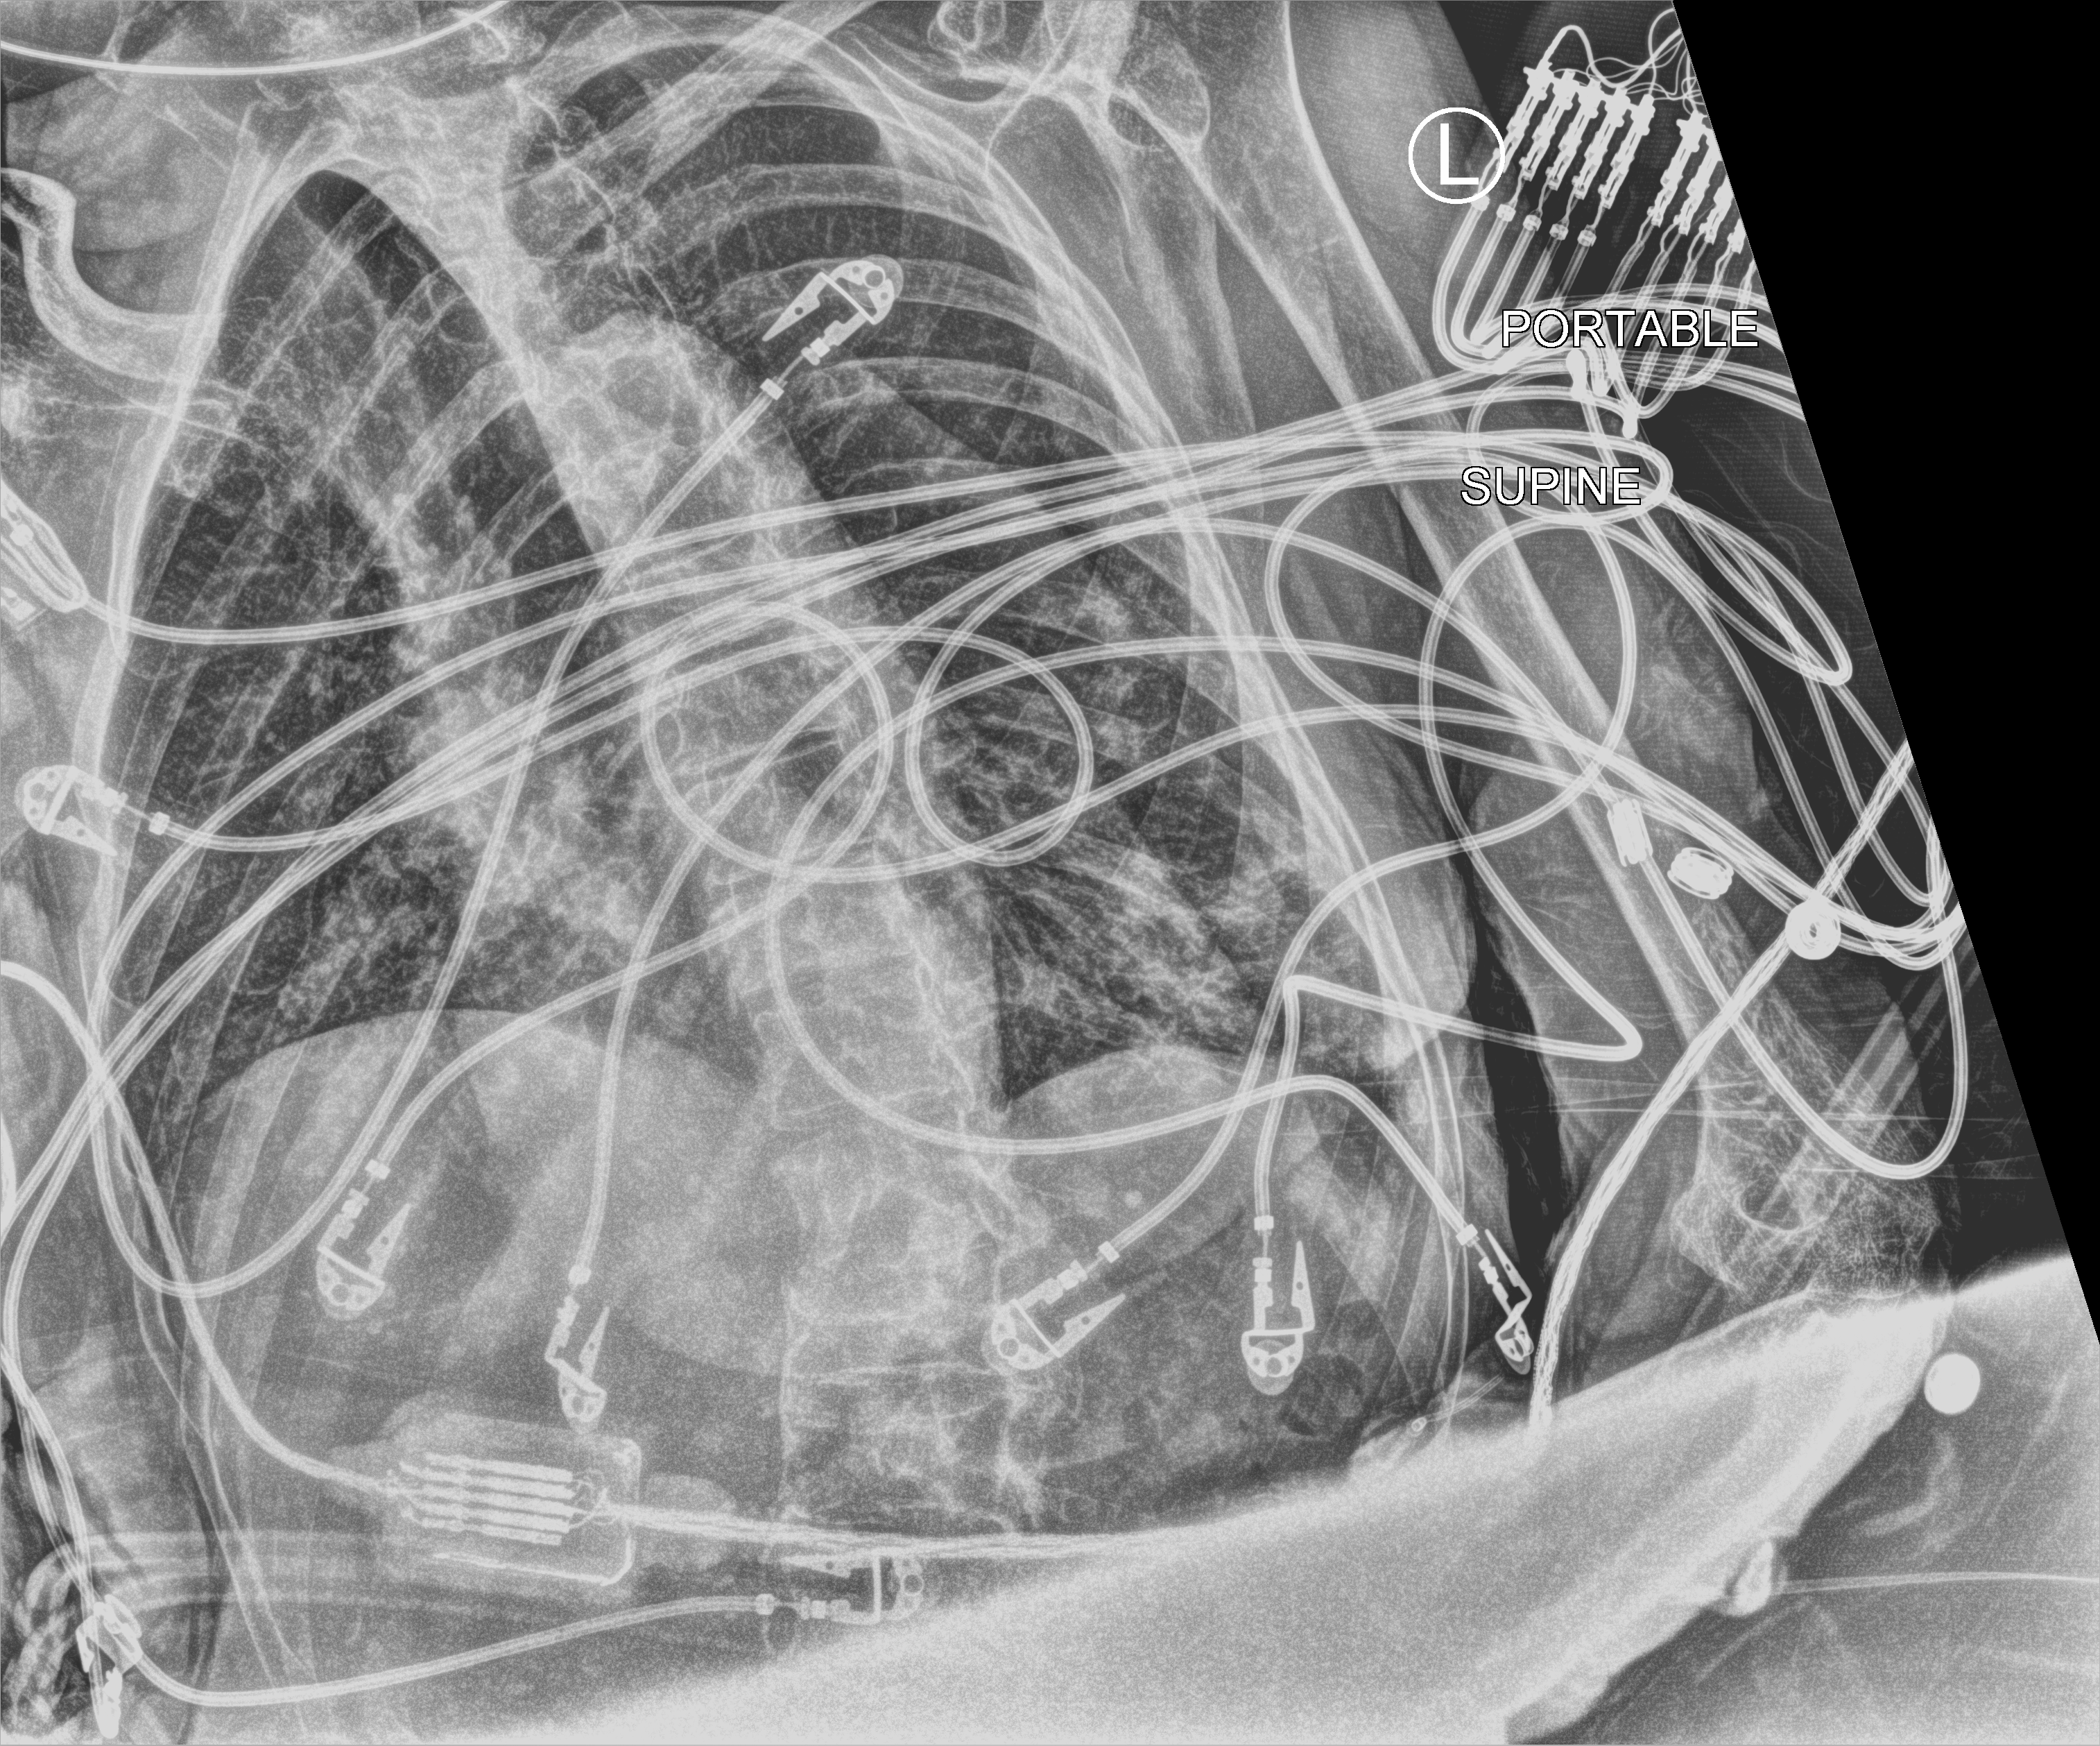
Portable chest radiograph, anteroposterior (AP) projection. Female patient hospitalised with COVID-19, age 75–90 years.
From the hospital-stay record, not from the radiograph (when in the stay this image was taken is not recorded): mechanically ventilated during this hospital stay: no.